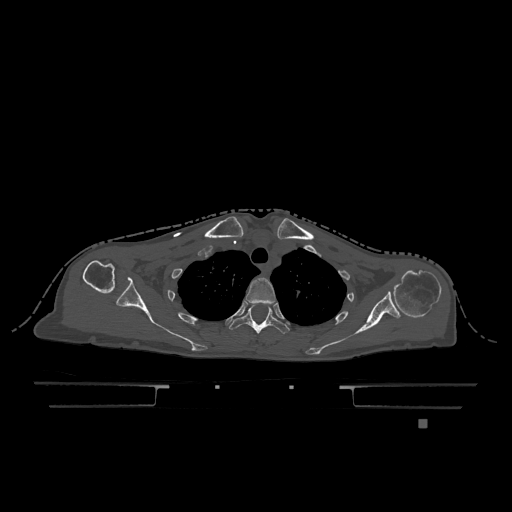
CT including the spine, one axial slice; position 938 of 1317 along the scan axis; bone window (W 1800 / L 400 HU); 0.5 mm slice thickness; 512 × 512 image matrix, field of view 500 × 500 mm. Female patient, age 74 years. Case-level facts recorded for this patient, not image findings: primary cancer: lung; vertebrae with lytic lesions (as recorded): T1, T4, T5, T6, L4, L5.
Annotated regions visible in this slice (semi-automatically segmented with operator editing):
- T2 vertebra: bounding box [x1, y1, x2, y2] px = [245, 278, 276, 304]
- T3 vertebra: [230, 306, 289, 334]